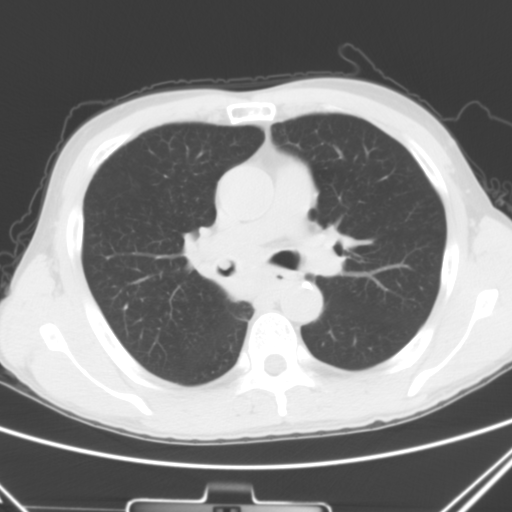
Chest CT, one axial slice; slice 29 of 51 in the series (ordered by position); 120 kVp; lung window (W 1500 / L -600 HU); 512 × 512 image matrix, field of view 327 × 327 mm. Male patient, age 52 years. Case-level facts recorded for this patient, not image findings: clinical TNM (as recorded): T2a N0 M1c.
Outlined on this slice (rectangle marked by the reading radiologist):
- lung tumour (recorded histology: squamous cell carcinoma): box from (x=182, y=223) to (x=251, y=313) px